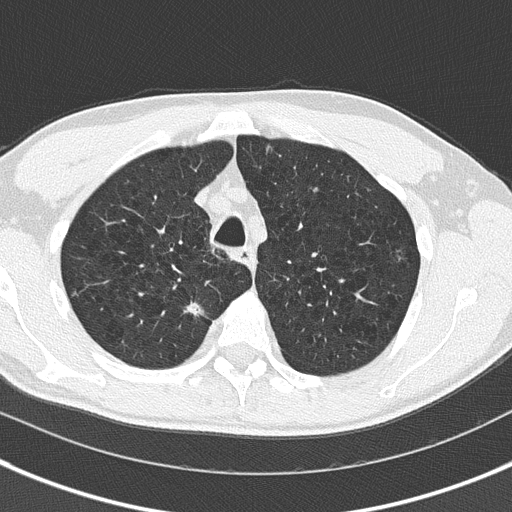
Low-dose screening chest CT, axial slice. Baseline screening round. Lung window (W 1500 / L -600 HU). 2 mm slice thickness. Lung (sharp) reconstruction kernel (B50f). 120 kVp. Slice 39 of 175 in the series. 512 × 512 image matrix. Male, age 56 years at enrolment. Current smoker at enrolment.
• Lesion marked by an expert reader, bounding box <178,293,223,336> (left, top, right, bottom; pixels).
• The screening reader recorded 3 non-calcified nodules or masses ≥4 mm on this exam (right upper lobe, right upper lobe, left lower lobe); which of them this box marks is not recorded.
• Official screen result: positive, change unspecified: nodule(s) >= 4 mm or enlarging nodule(s), mass(es), or other non-specific abnormalities suspicious for lung cancer.
• Lung cancer was diagnosed 228 days after this screen: non-small cell carcinoma, right upper lobe, stage IIIA (AJCC 6th edition), 21 mm at pathology.